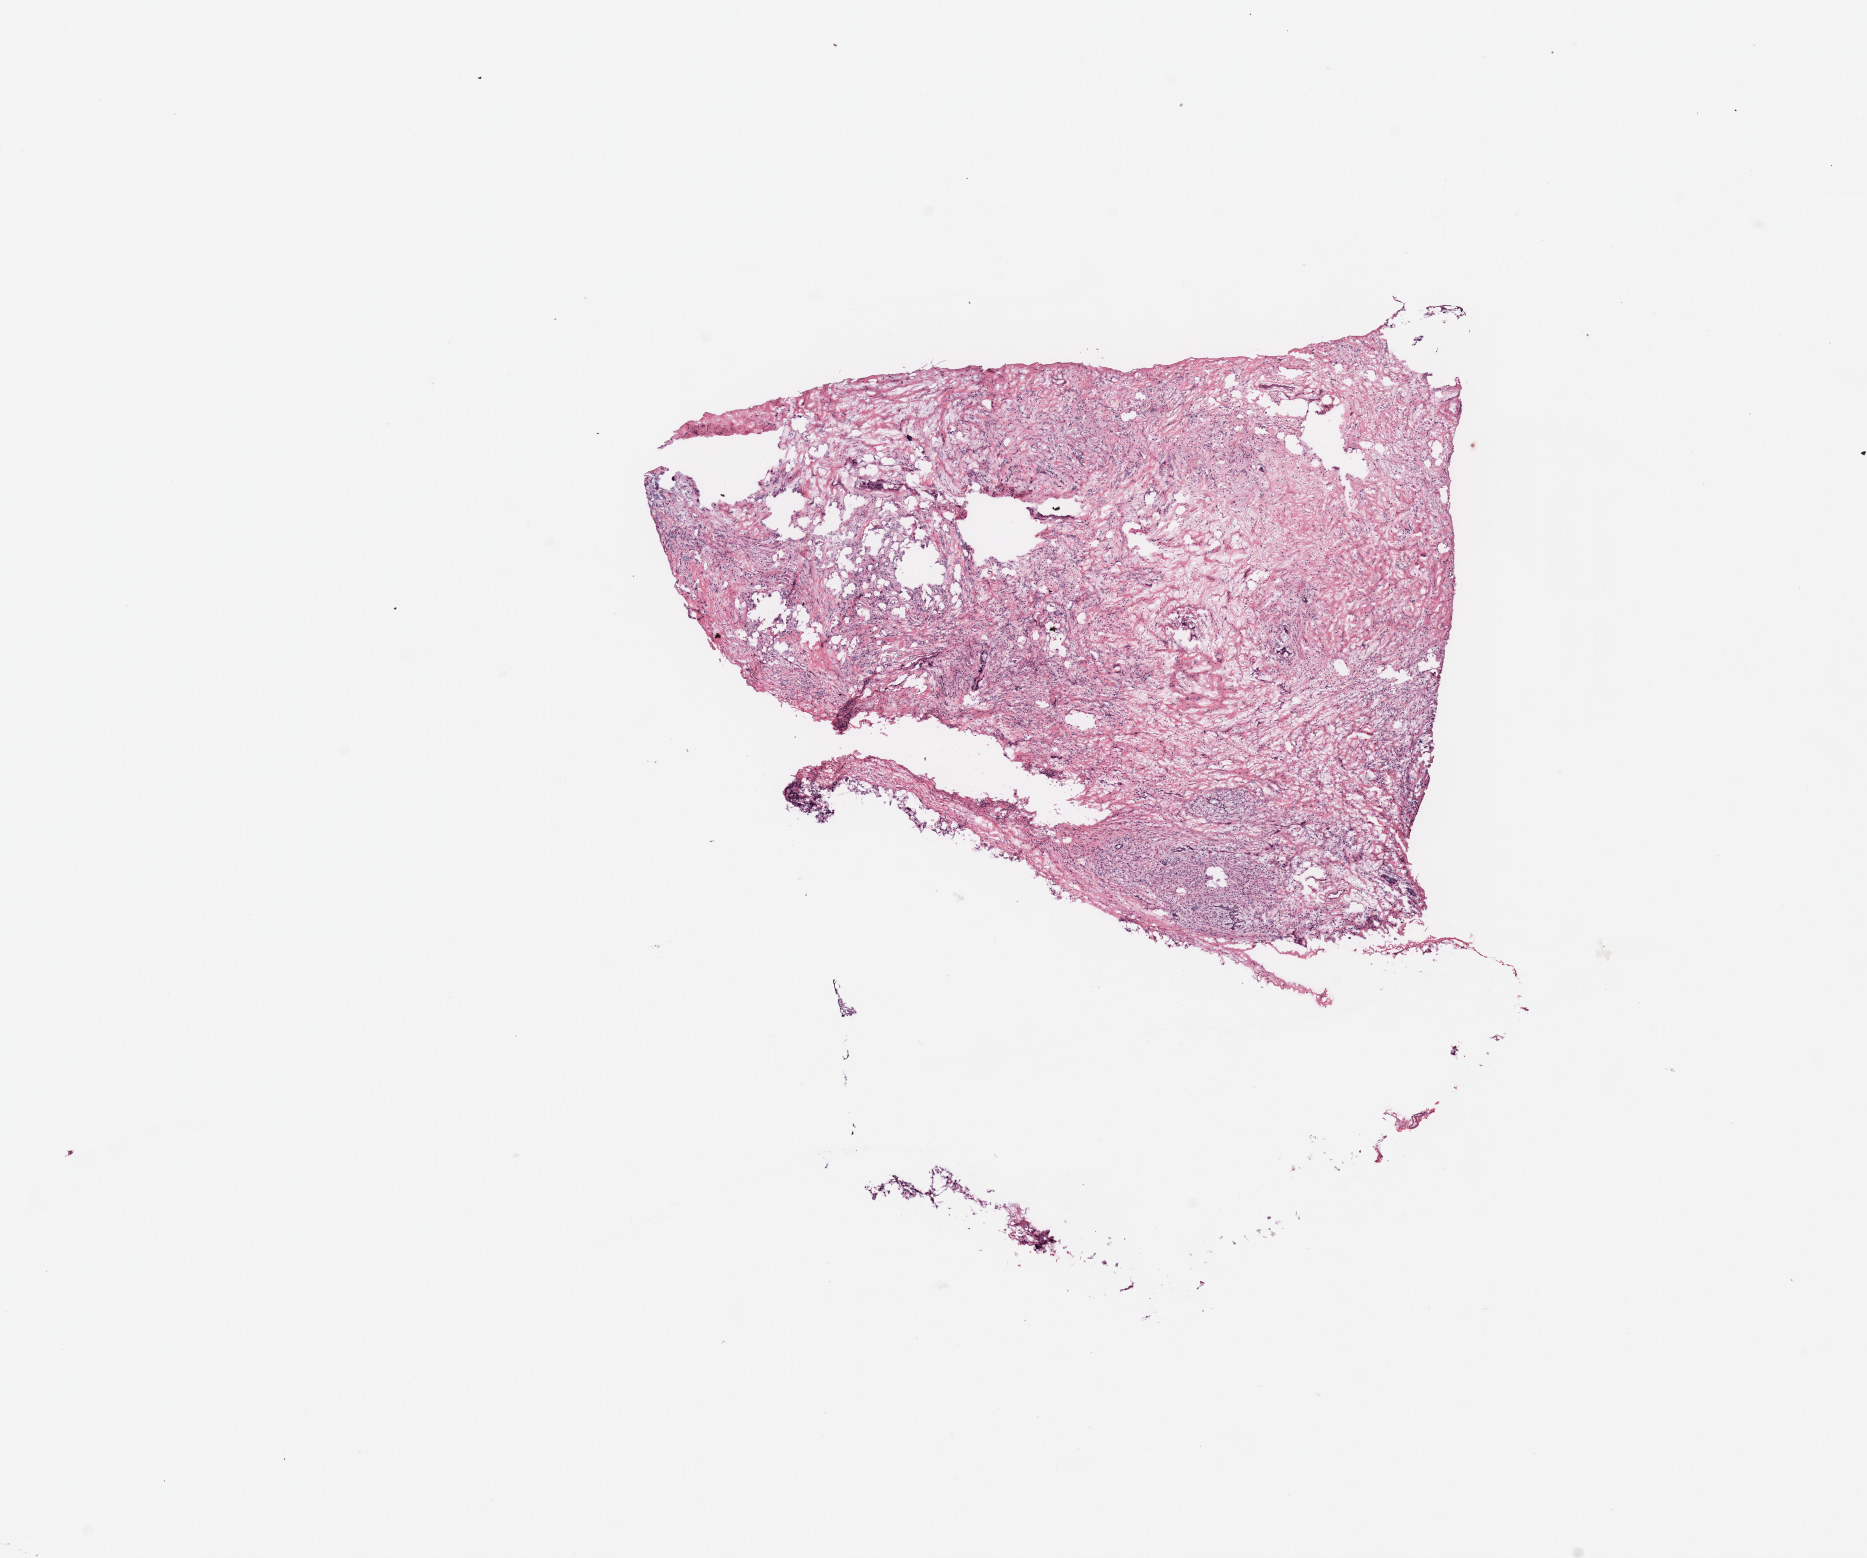
Whole-slide histology image, H&E, shown as a low-resolution overview of the whole scanned area (about 14.8 x 12.3 mm, from a 20x scan); tumour tissue sample, breast. Patient: female, age 71 years.
Diagnosis: Infiltrating lobular carcinoma, NOS.